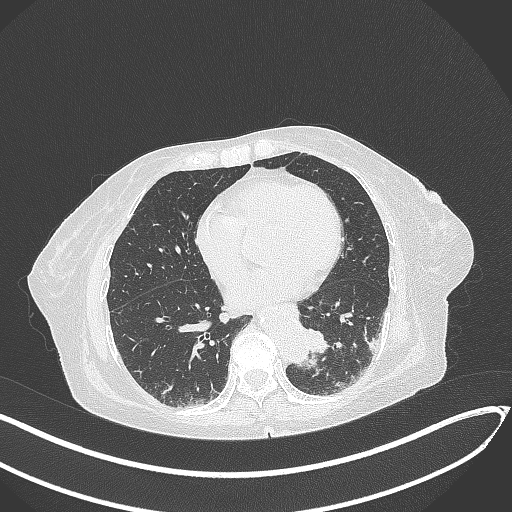
Chest CT, one axial slice; position 85 of 324 along the scan axis; reconstruction kernel B70f; lung window (W 1500 / L -600 HU); 1 mm slice thickness; 512 × 512 image matrix, field of view 400 × 400 mm. Patient: female, 82 years. Case-level facts recorded for this patient, not image findings: clinical TNM (as recorded): T1b N0 M1.
Structures marked on this image (bounding box drawn by a radiologist):
- lung tumour (recorded histology: adenocarcinoma): bounding box <301,324,332,357> (left, top, right, bottom; pixels)